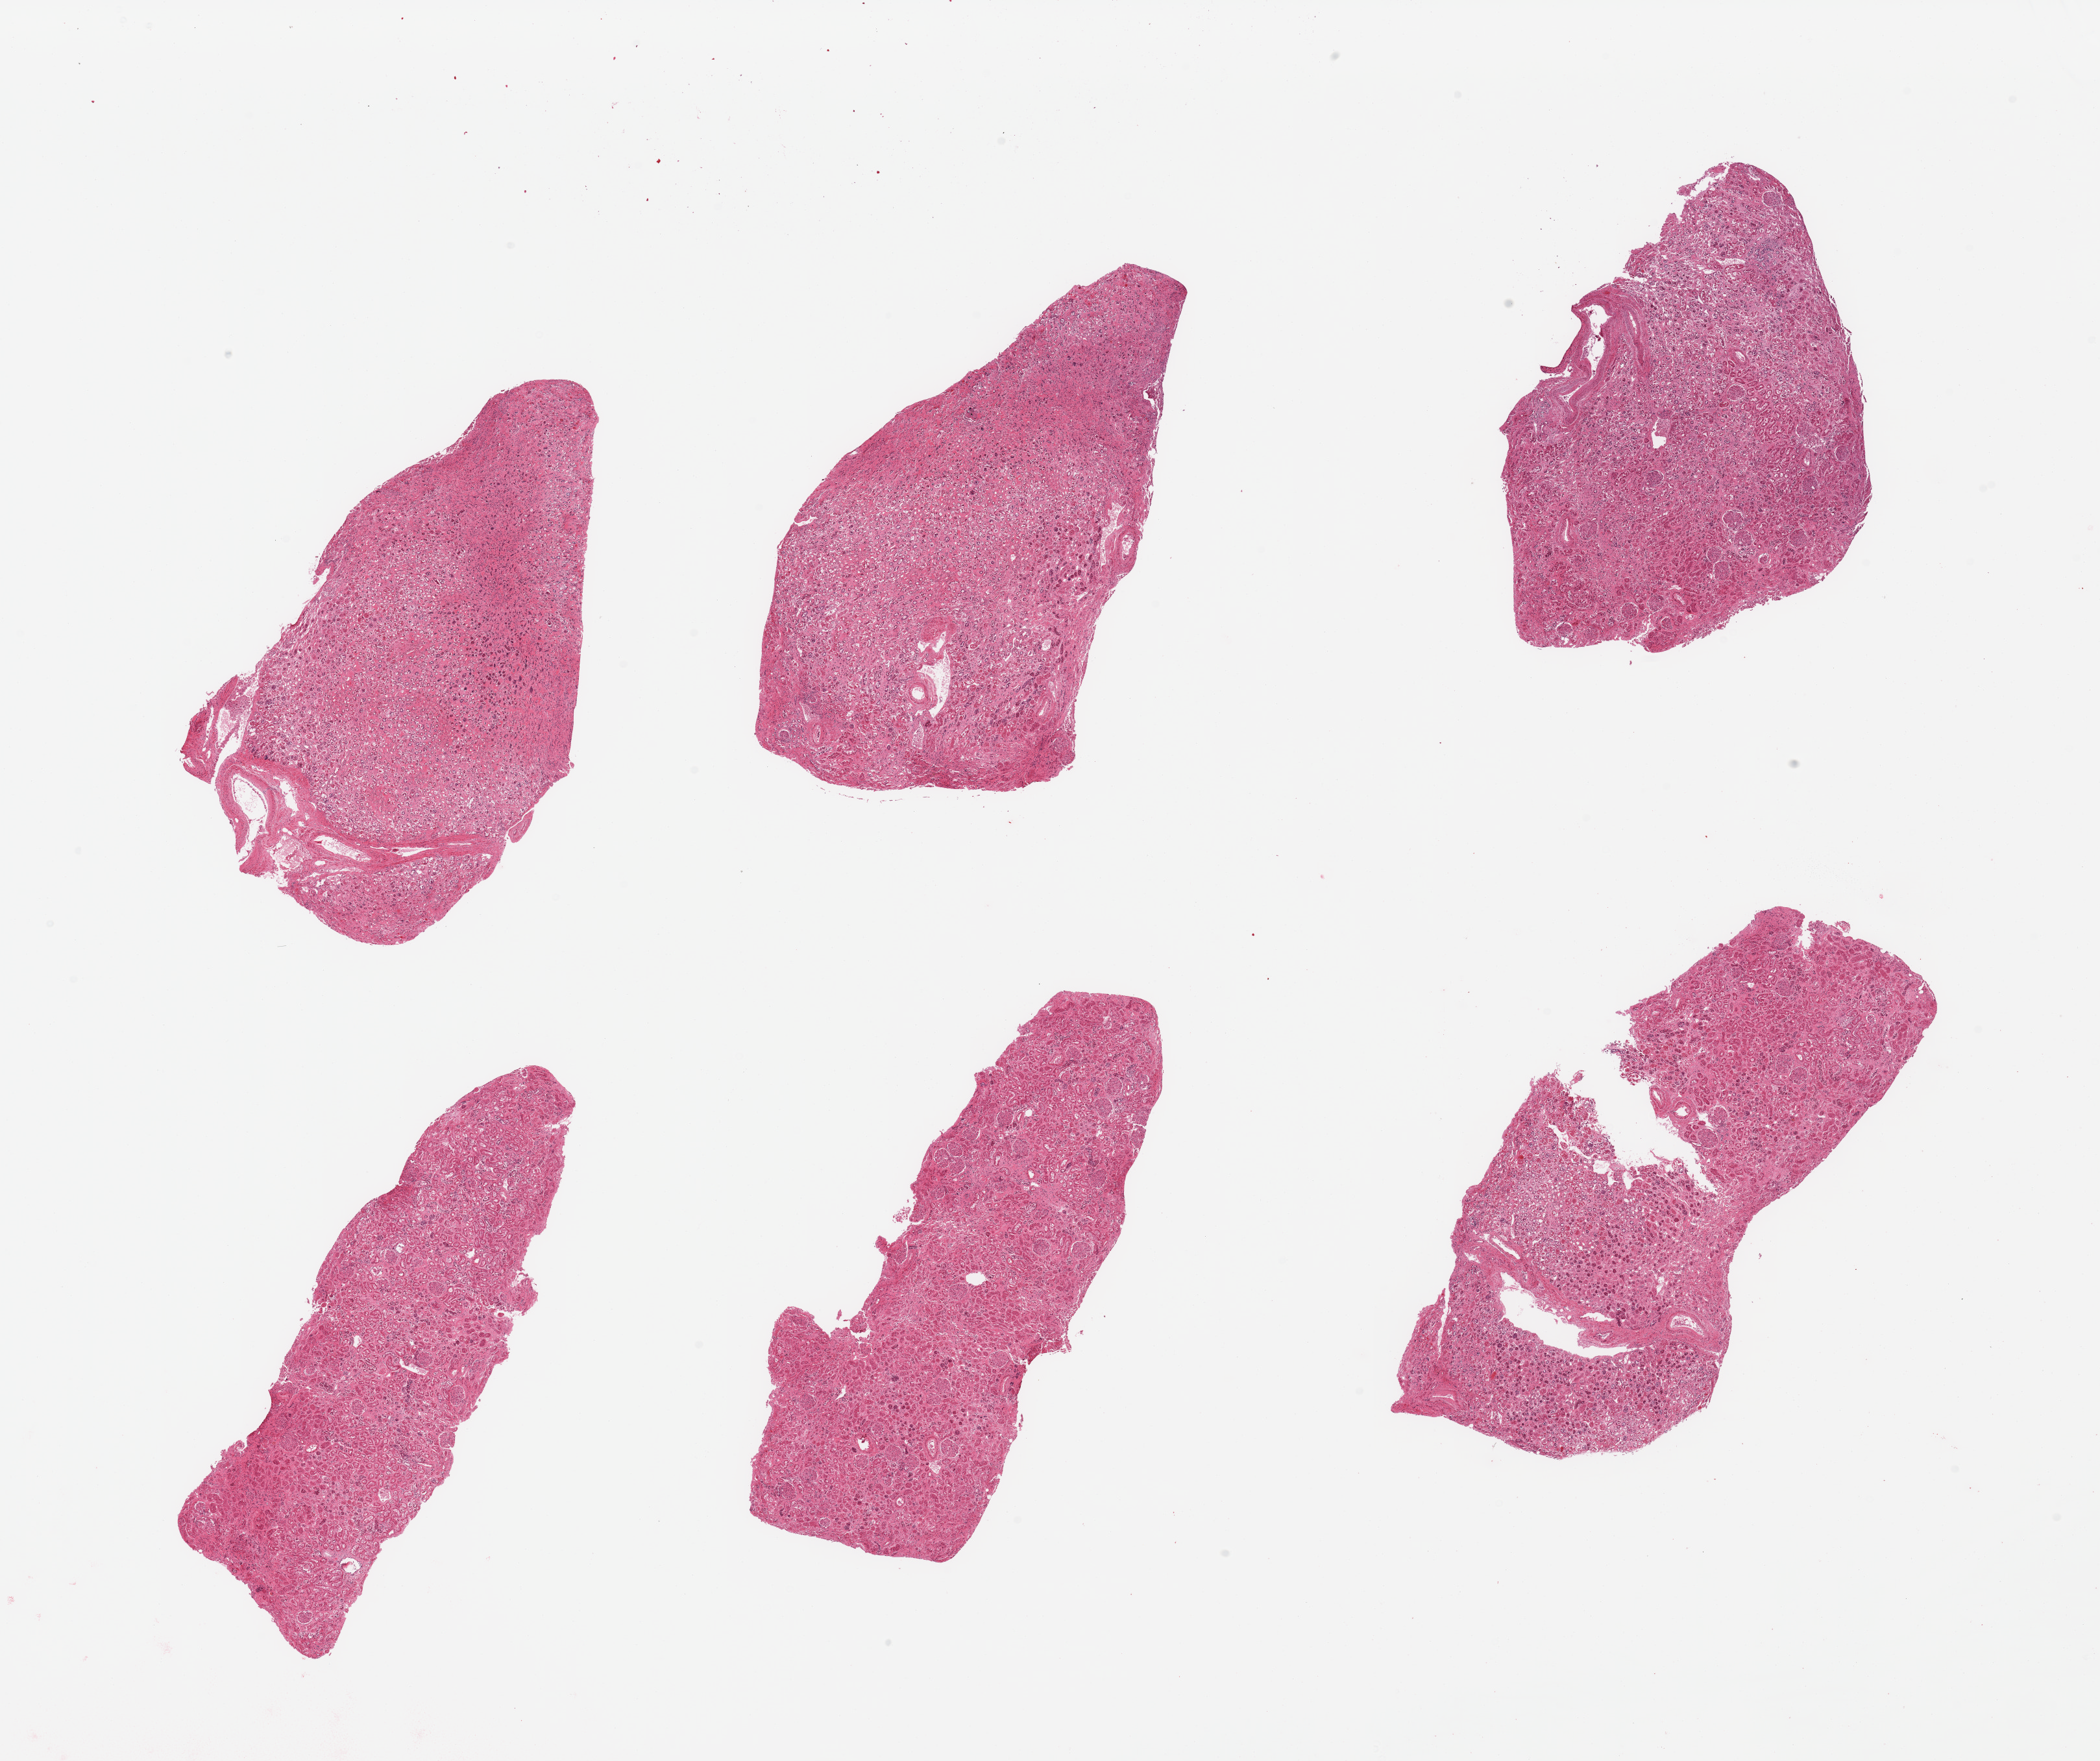
Digitized hematoxylin and eosin (H&E)-stained section — a low-resolution overview of the entire scanned area, about 25.6 x 21.5 mm (acquisition: 20x scan). PAXgene-fixed, paraffin-embedded tissue. Section of renal cortex (target tissue). Donor tissue sample.
Reviewer comment on this tissue sample: 6 pieces; moderately autolyzed, include significant portion of medulla.